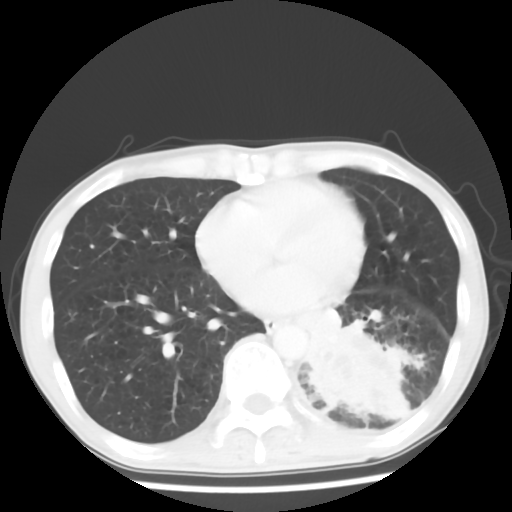
Chest CT, one axial slice; position 23 of 64 along the scan axis; reconstruction kernel STANDARD; 120 kVp; lung window (W 1500 / L -600 HU); 5 mm slice thickness; 512 × 512 image matrix, field of view 313 × 313 mm. Patient: male, 68 years. From the clinical record (not read from this slice): clinical TNM (as recorded): T4 N0 M0.
Structures marked on this image (rectangle marked by the reading radiologist):
- lung tumour (recorded histology: squamous cell carcinoma): bounding box [x1, y1, x2, y2] px = [300, 316, 413, 438]